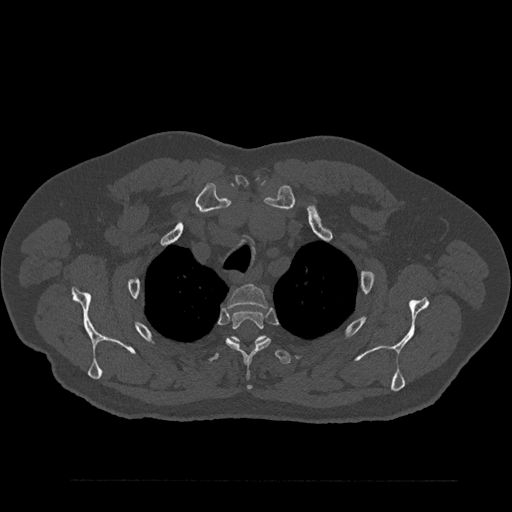
CT including the spine, one axial slice; position 681 of 797 along the scan axis; 120 kVp; bone window (W 1800 / L 400 HU); 512 × 512 image matrix. Male patient, age 61 years. From the clinical record (not read from this slice): primary cancer: prostate.
Structures marked on this image (semi-automatic segmentation, software-assisted and operator-edited):
- T2 vertebra: bounding box <228,285,267,308> (left, top, right, bottom; pixels)
- T3 vertebra: <225,310,271,390>
- T4 vertebra: <207,336,291,364>